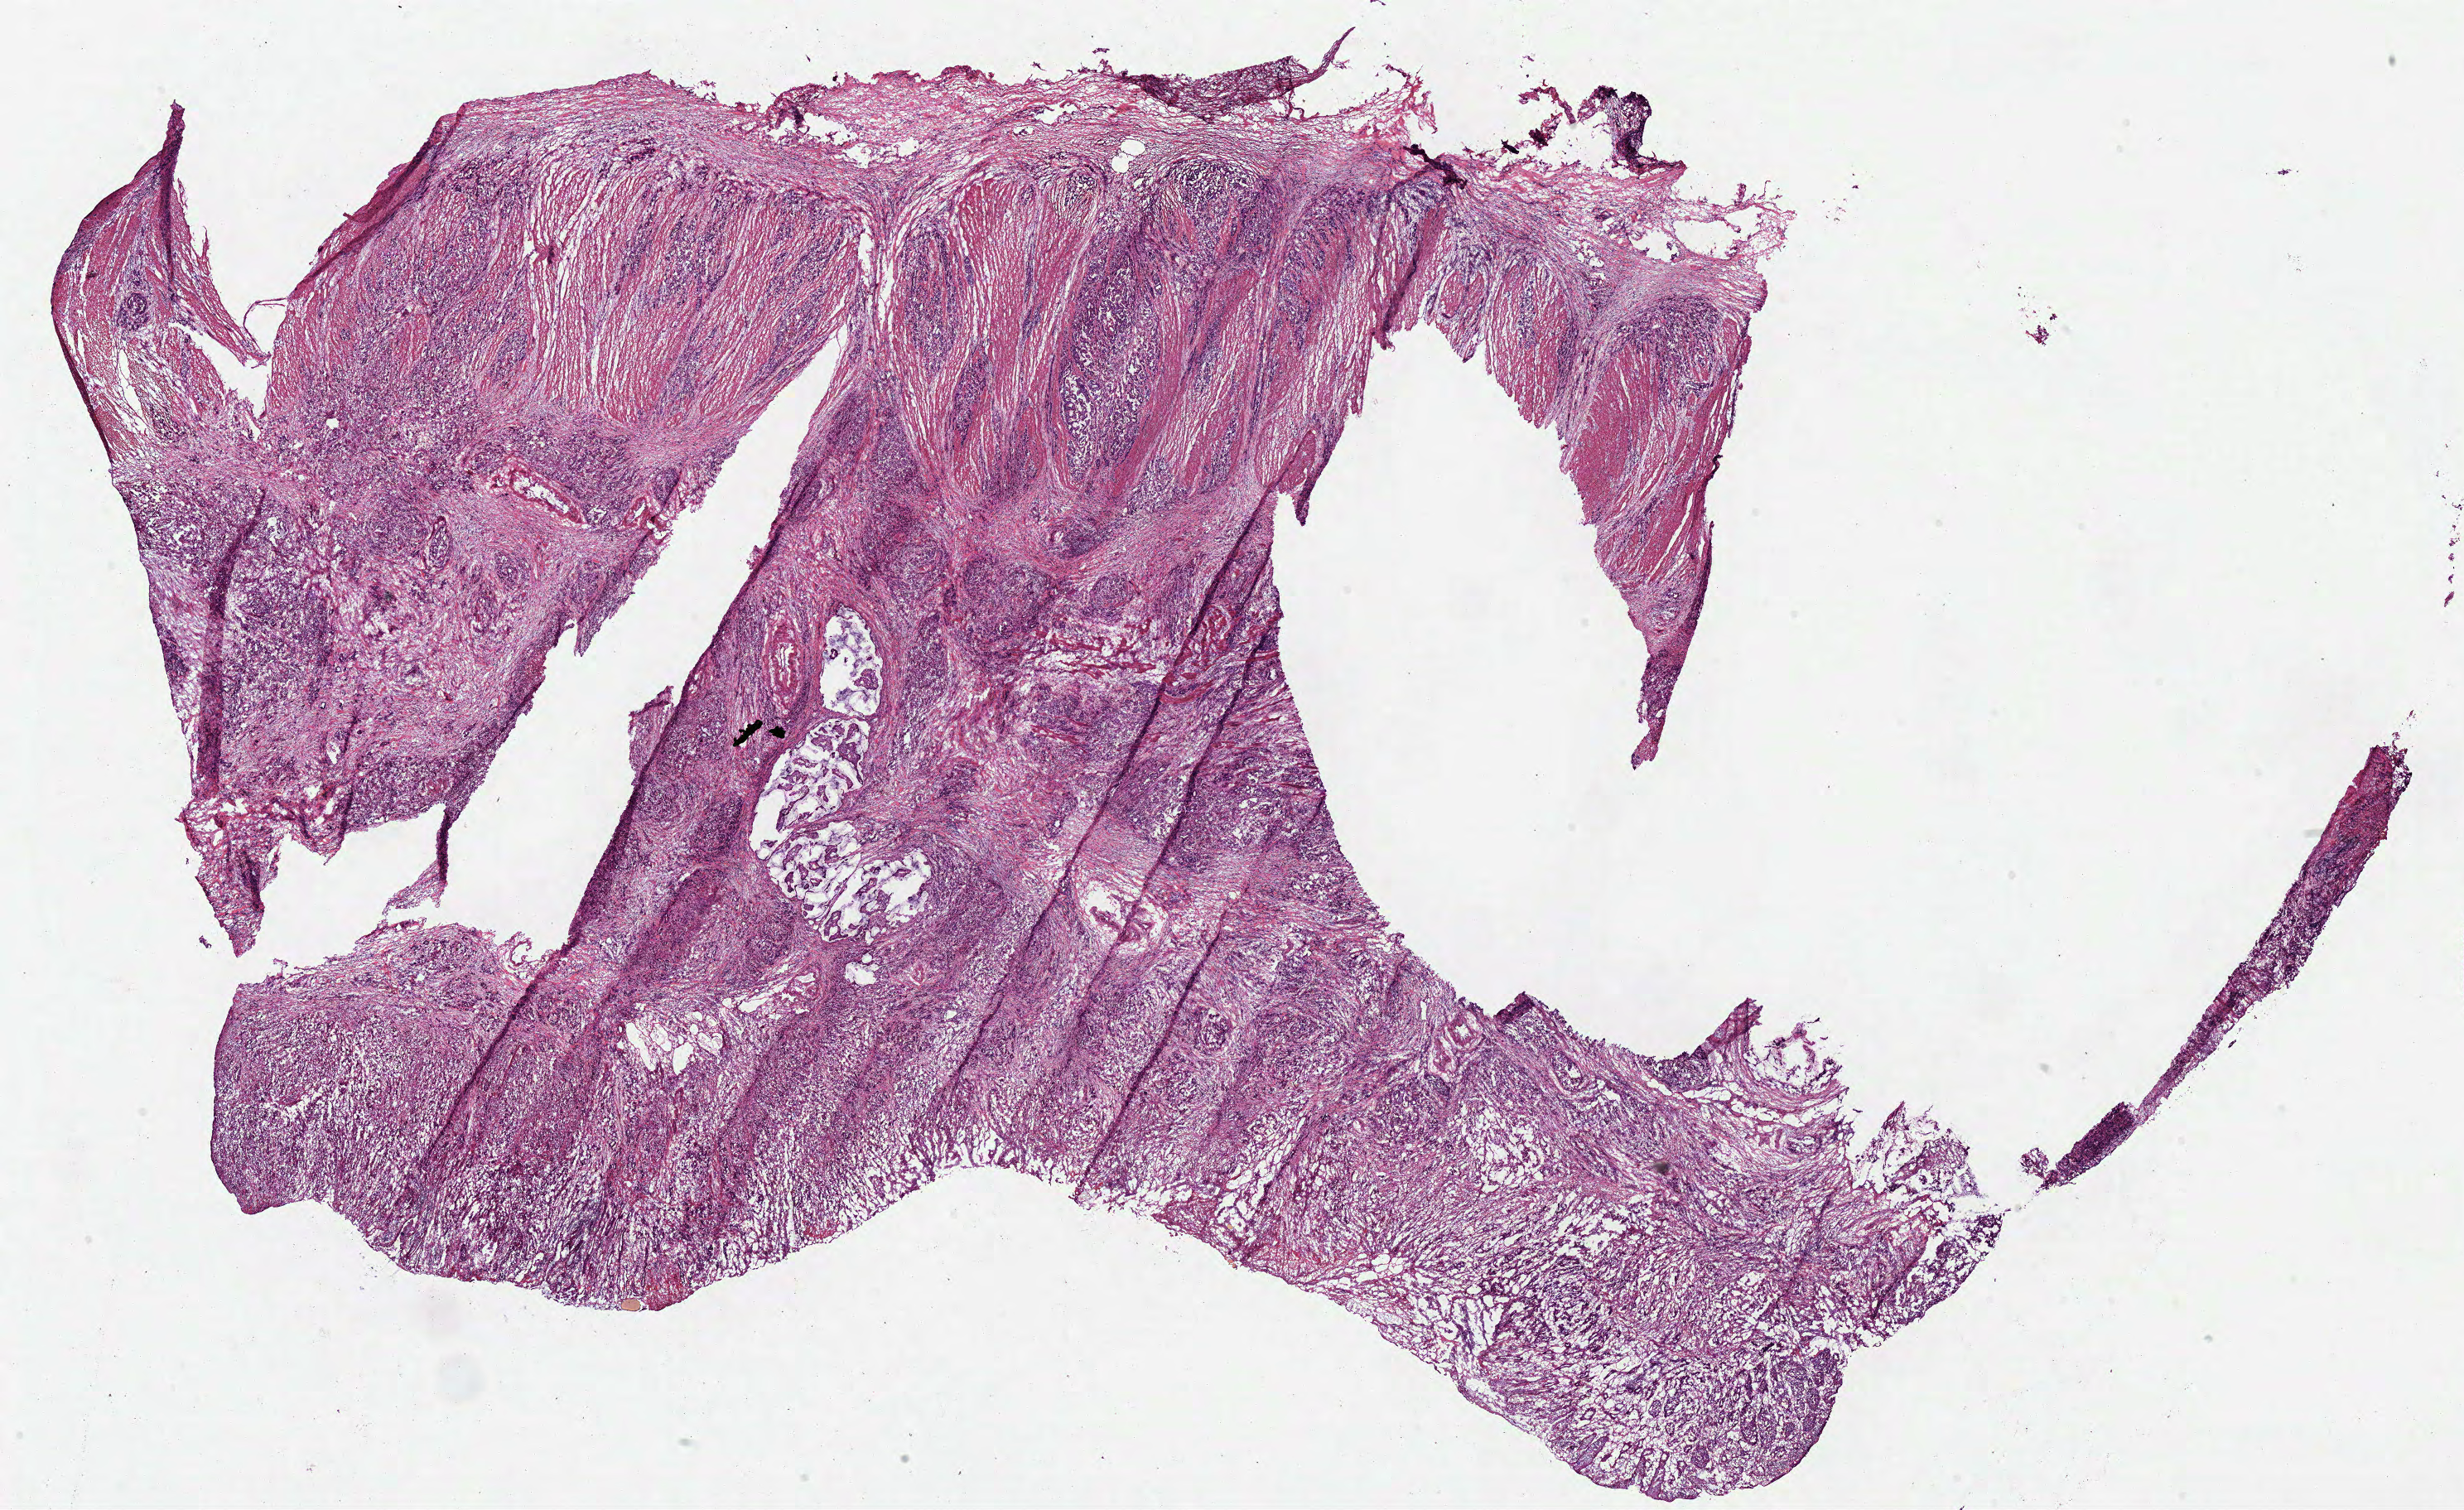
Whole-slide histology image, H&E, low-resolution overview of the scanned area, about 23.4 x 14.4 mm. Frozen section from the bottom of the tissue portion. Rectum, primary tumour sample. Female patient; age at initial diagnosis 77 years. Composition of this section per pathologist review: tumour cells 97%, tumour nuclei 75%, normal cells 1%, stromal cells 0%, necrosis 2%. Inflammatory infiltration, as recorded: lymphocyte infiltration 5%, monocyte infiltration 0%, neutrophil infiltration 5%.
Lymph nodes positive (case pathology): 4 of 4 examined. TNM: T4b N2a M0. AJCC pathologic stage: IIIC (7th edition). Pathologic diagnosis: Adenocarcinoma, NOS (rectosigmoid junction).